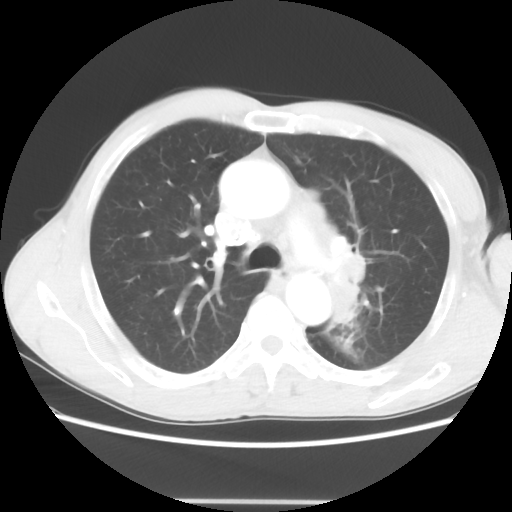
Chest CT, one axial slice. Position 43 of 62 along the scan axis. Reconstruction kernel STANDARD. 100 kVp. Lung window (W 1500 / L -600 HU). 512 × 512 image matrix, field of view 360 × 360 mm. Male patient, age 61 years. Case-level facts recorded for this patient, not image findings: clinical TNM (as recorded): T3 N1 M1.
Structures marked on this image (bounding box drawn by a radiologist):
- lung tumour (recorded histology: adenocarcinoma): bounding box <300,186,376,328> (left, top, right, bottom; pixels)